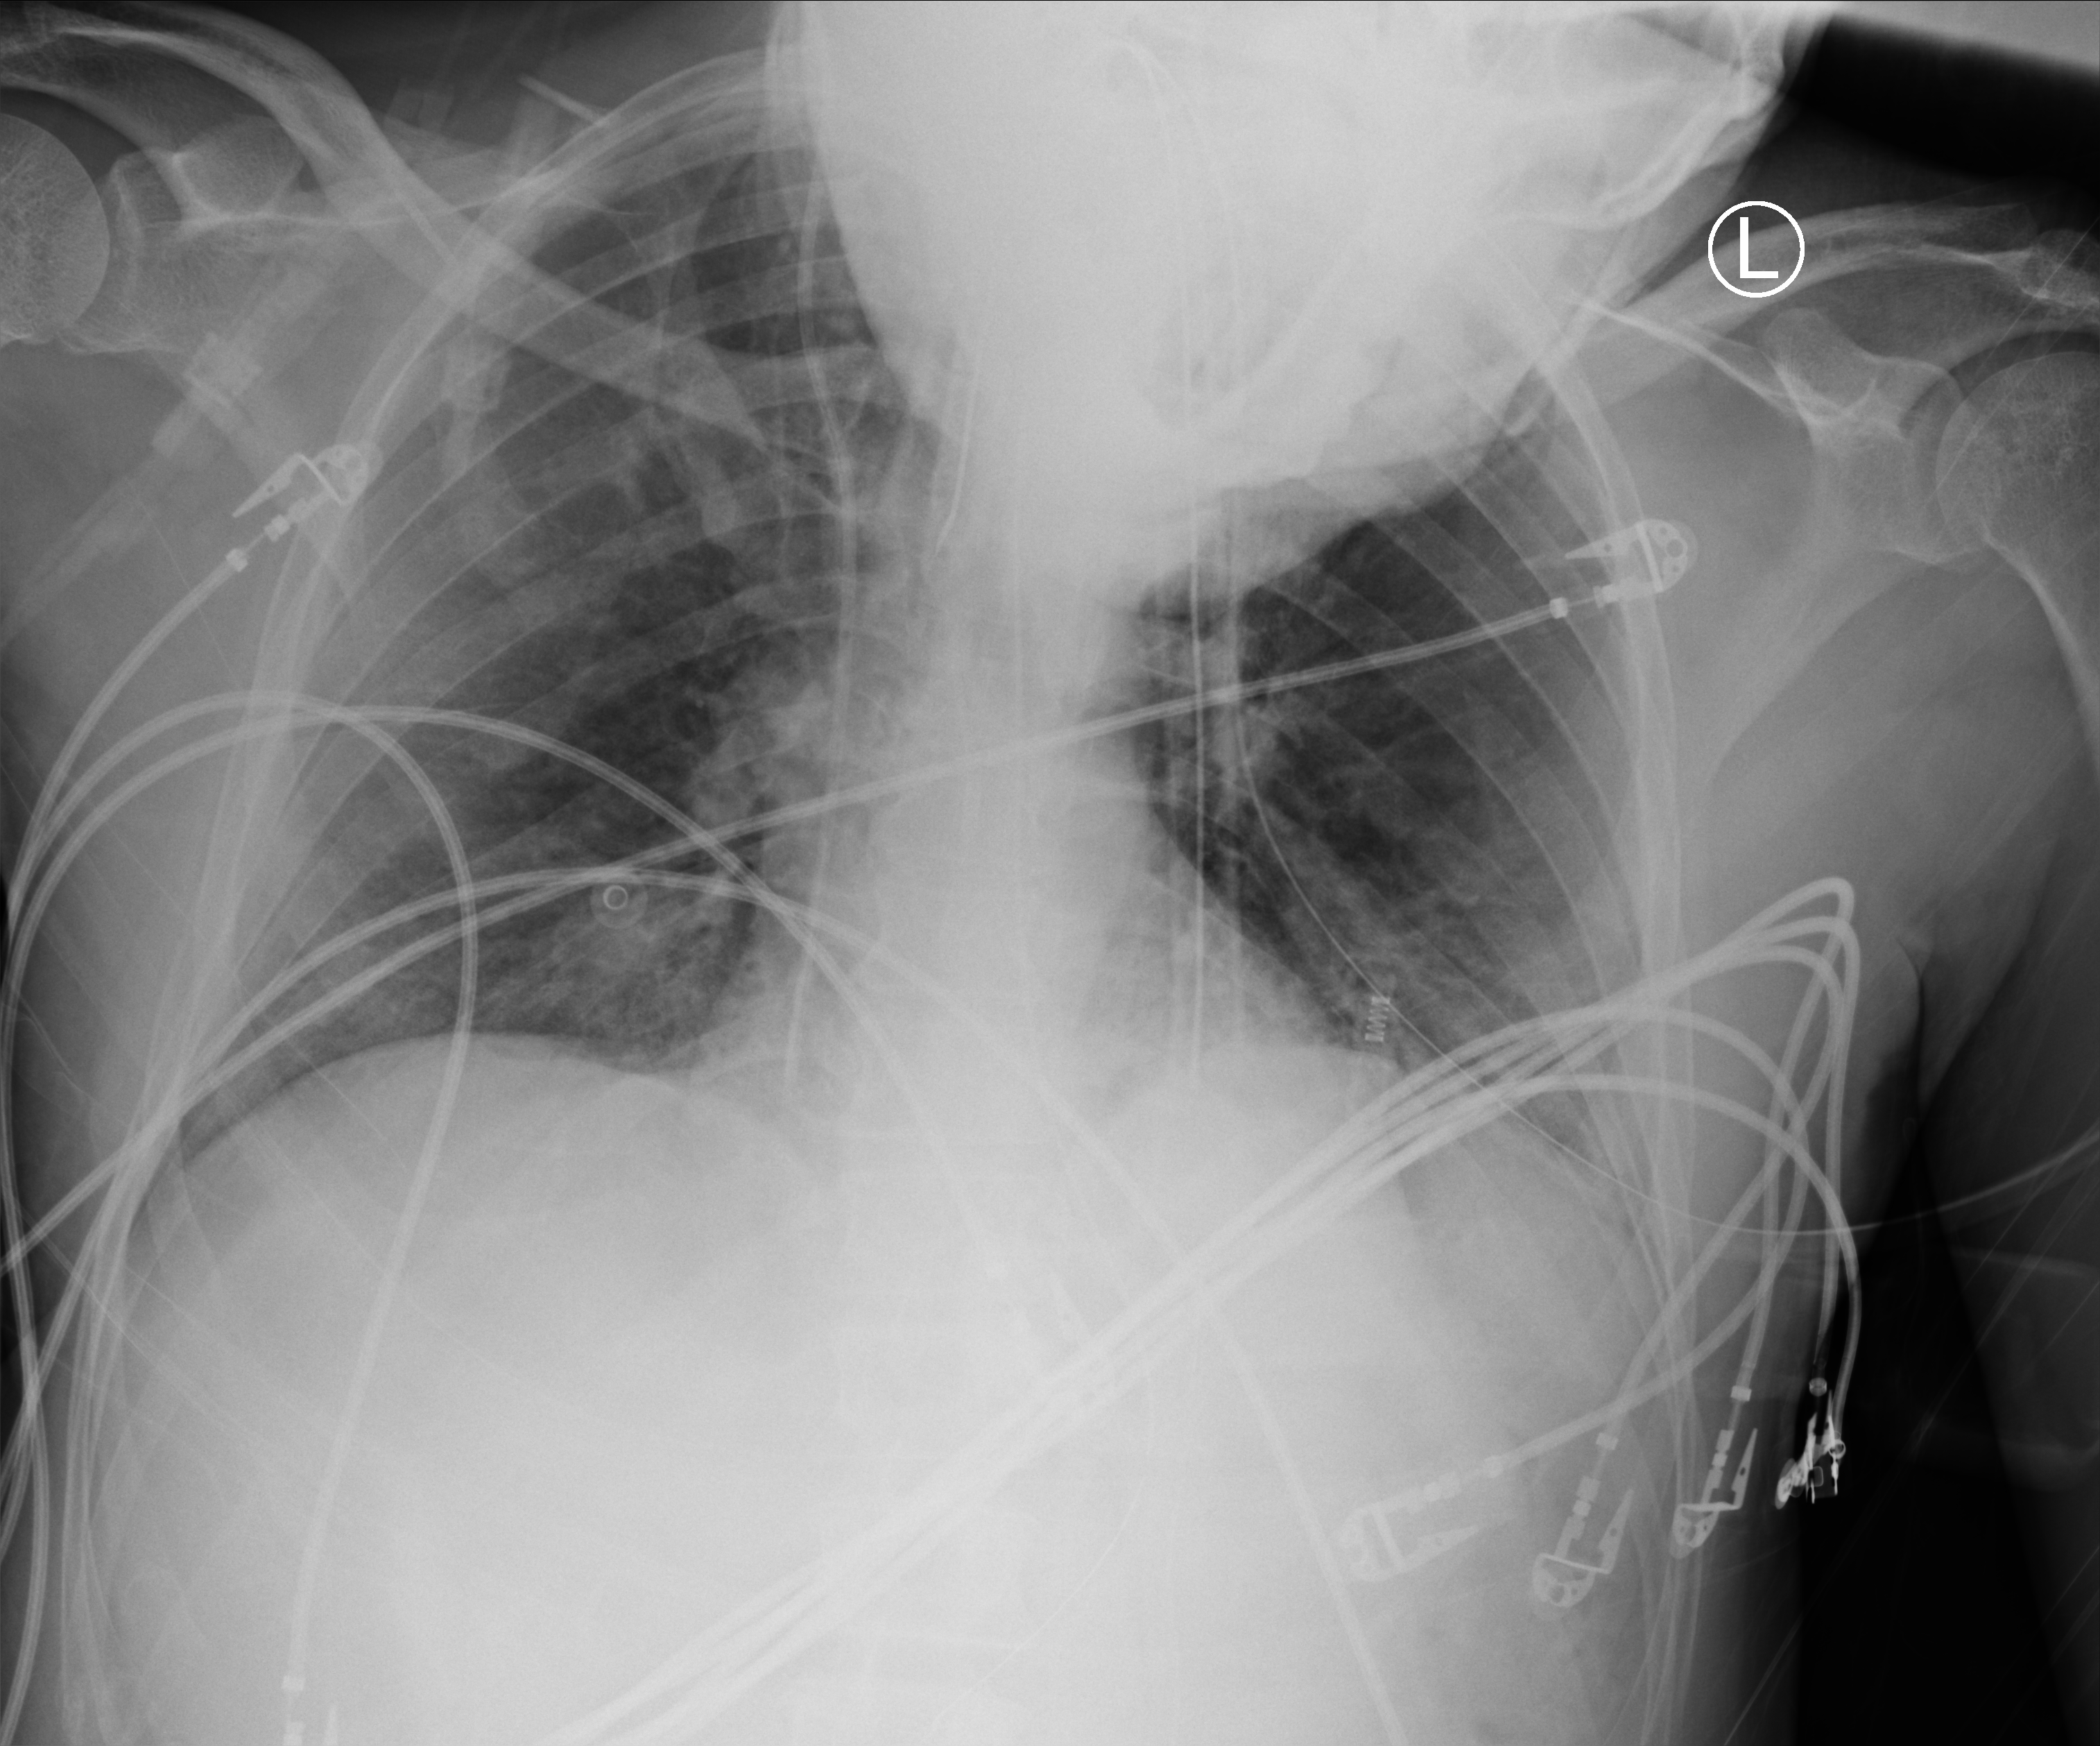
Bedside chest radiograph (computed radiography); anteroposterior (AP) projection. Male patient hospitalised with COVID-19, age 18–59 years.
From the hospital-stay record, not from the radiograph (when in the stay this image was taken is not recorded): other chronic lung disease (admission record): no; mechanically ventilated during this hospital stay: yes; length of hospital stay: 41 days.